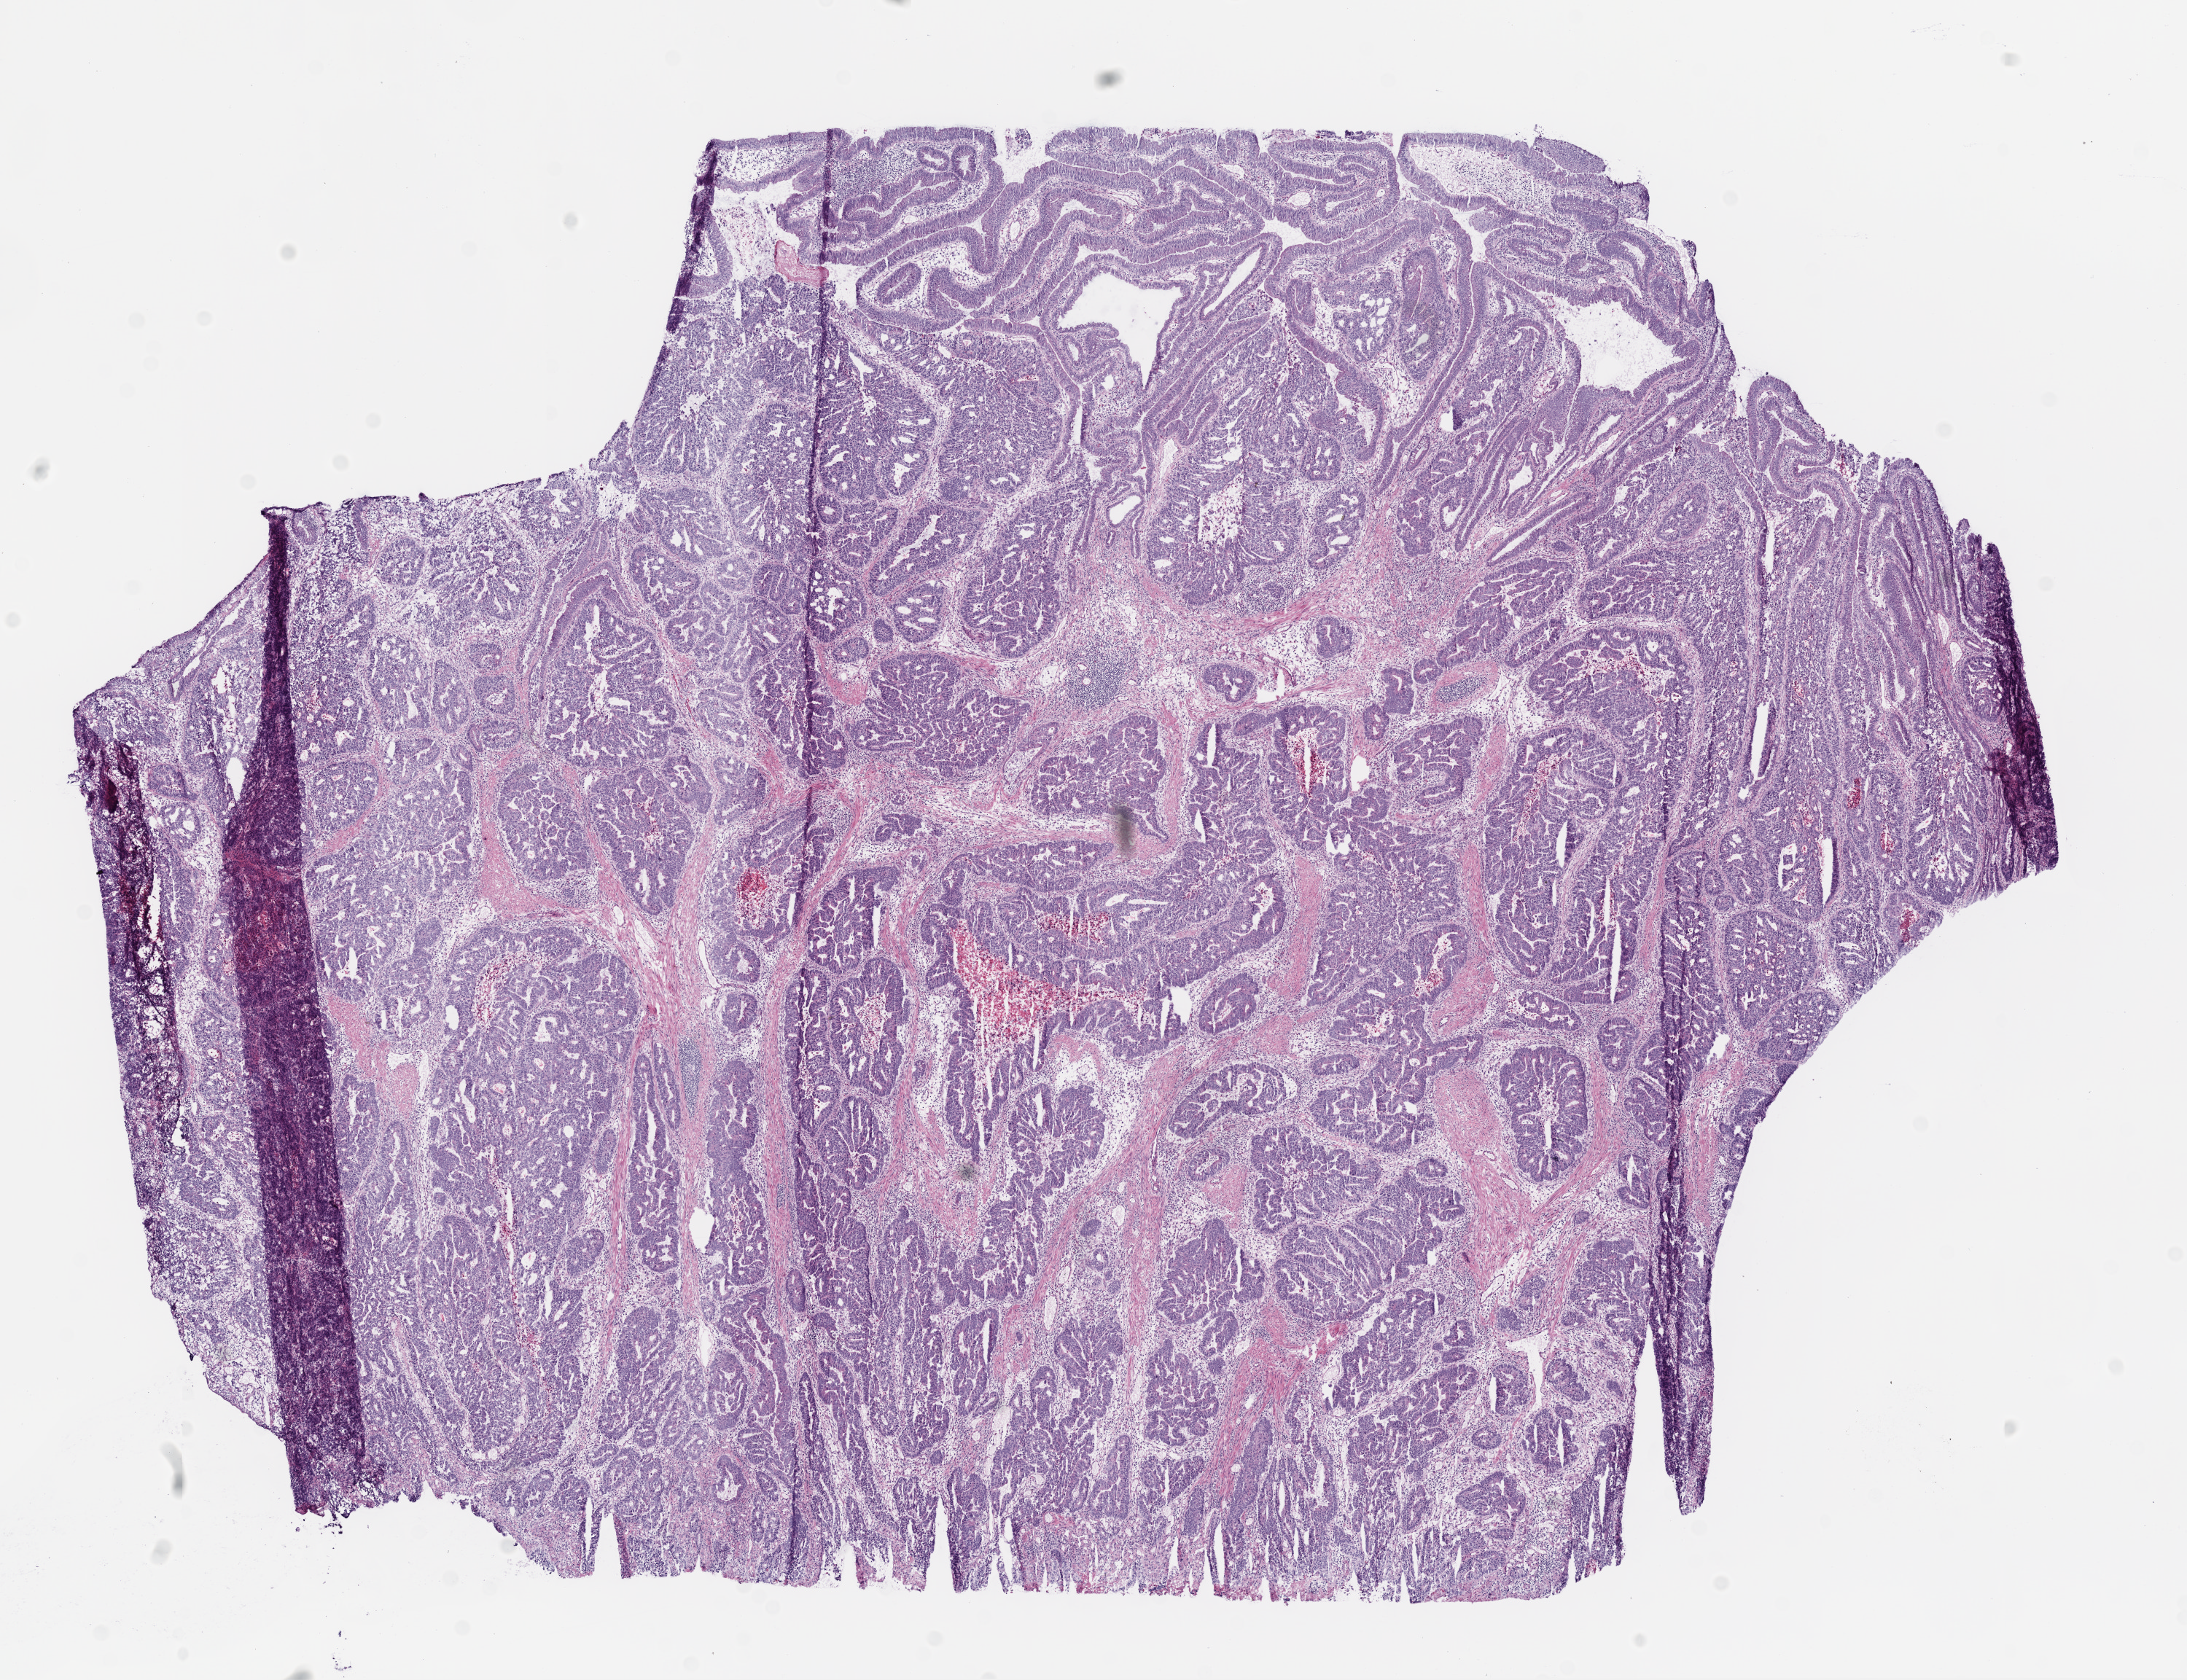
H&E-stained whole-slide image, a low-resolution overview of the entire scanned area, about 12.0 x 9.2 mm (slide scanned at 20x), frozen section from the bottom of the tissue portion, primary tumour sample from the rectum. Patient: female, age at initial diagnosis 41 years. Slide review estimates, as recorded: tumour cells 85%, tumour nuclei 80%, normal cells 0%, stromal cells 10%, necrosis 5%.
Pathologic diagnosis: Adenocarcinoma, NOS. AJCC pathologic stage: IV. Lymph nodes positive (case pathology): 6 of 32 examined.